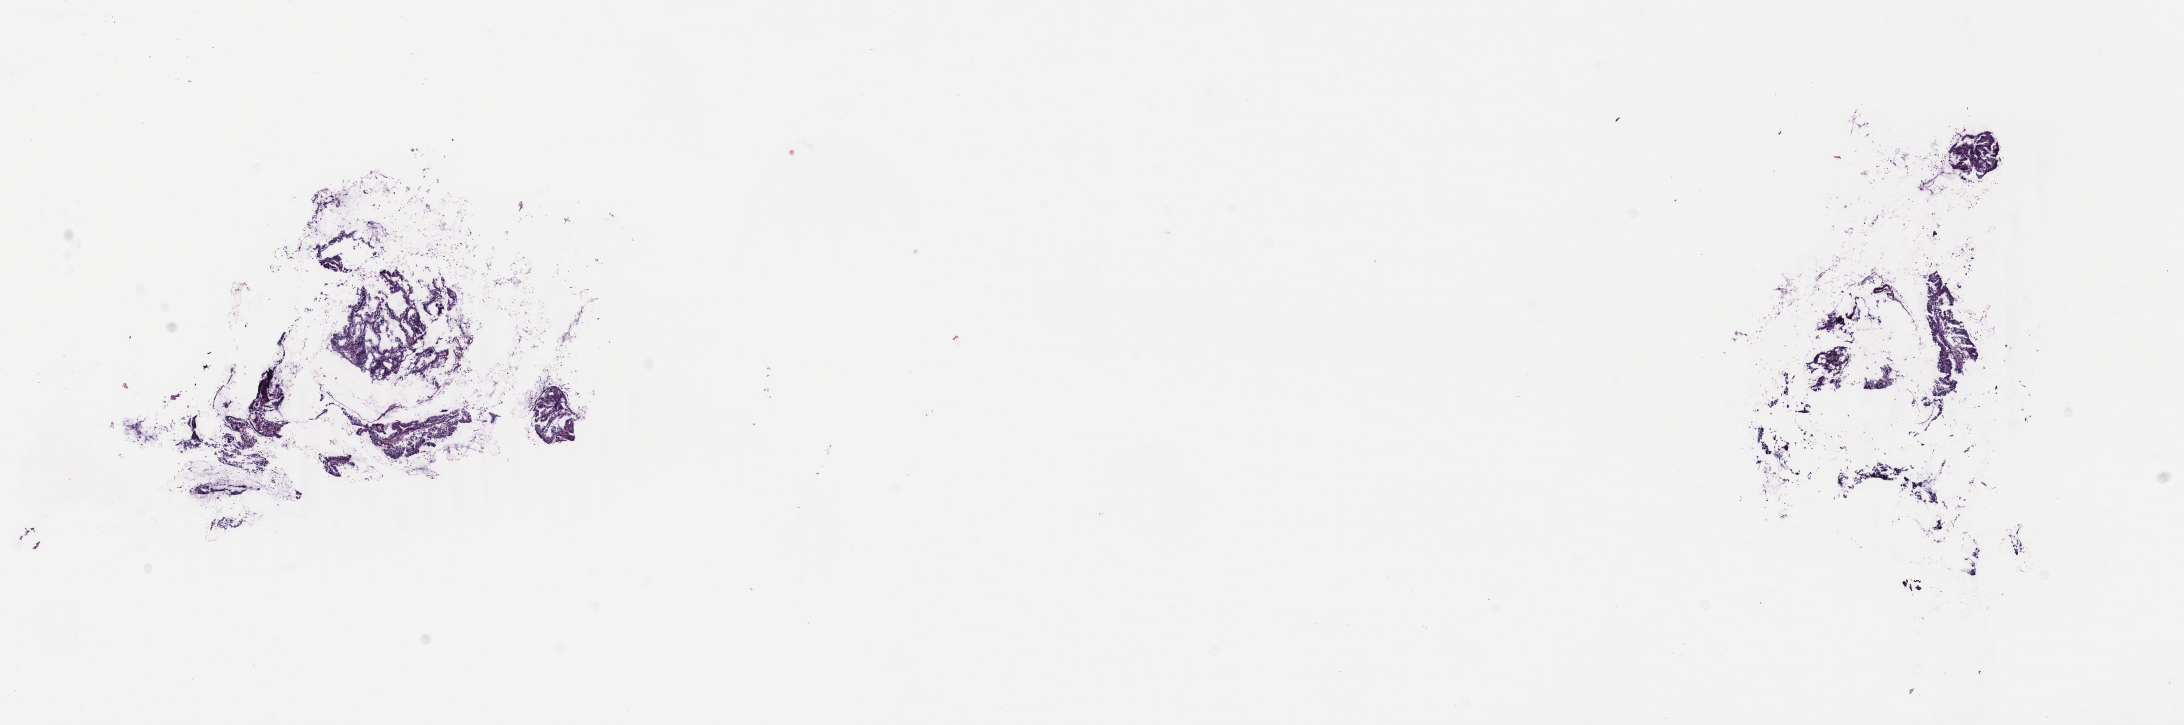
H&E whole-slide image — shown as a low-resolution overview of the whole scanned area (about 17.4 x 5.8 mm, from a 40x scan). Frozen section from the top of the tissue portion. Uterus, primary tumour sample. Female patient; age at initial diagnosis 69 years. Histologic grade: G1 (well differentiated). Composition of this section per pathologist review: tumour cells 90%, tumour nuclei 90%, normal cells 0%, stromal cells 10%, necrosis 0%. Inflammatory infiltration, as recorded: lymphocyte infiltration 50%, monocyte infiltration 10%, neutrophil infiltration 20%.
• FIGO stage: IB
• histologic diagnosis: Endometrioid adenocarcinoma, NOS (fundus uteri)